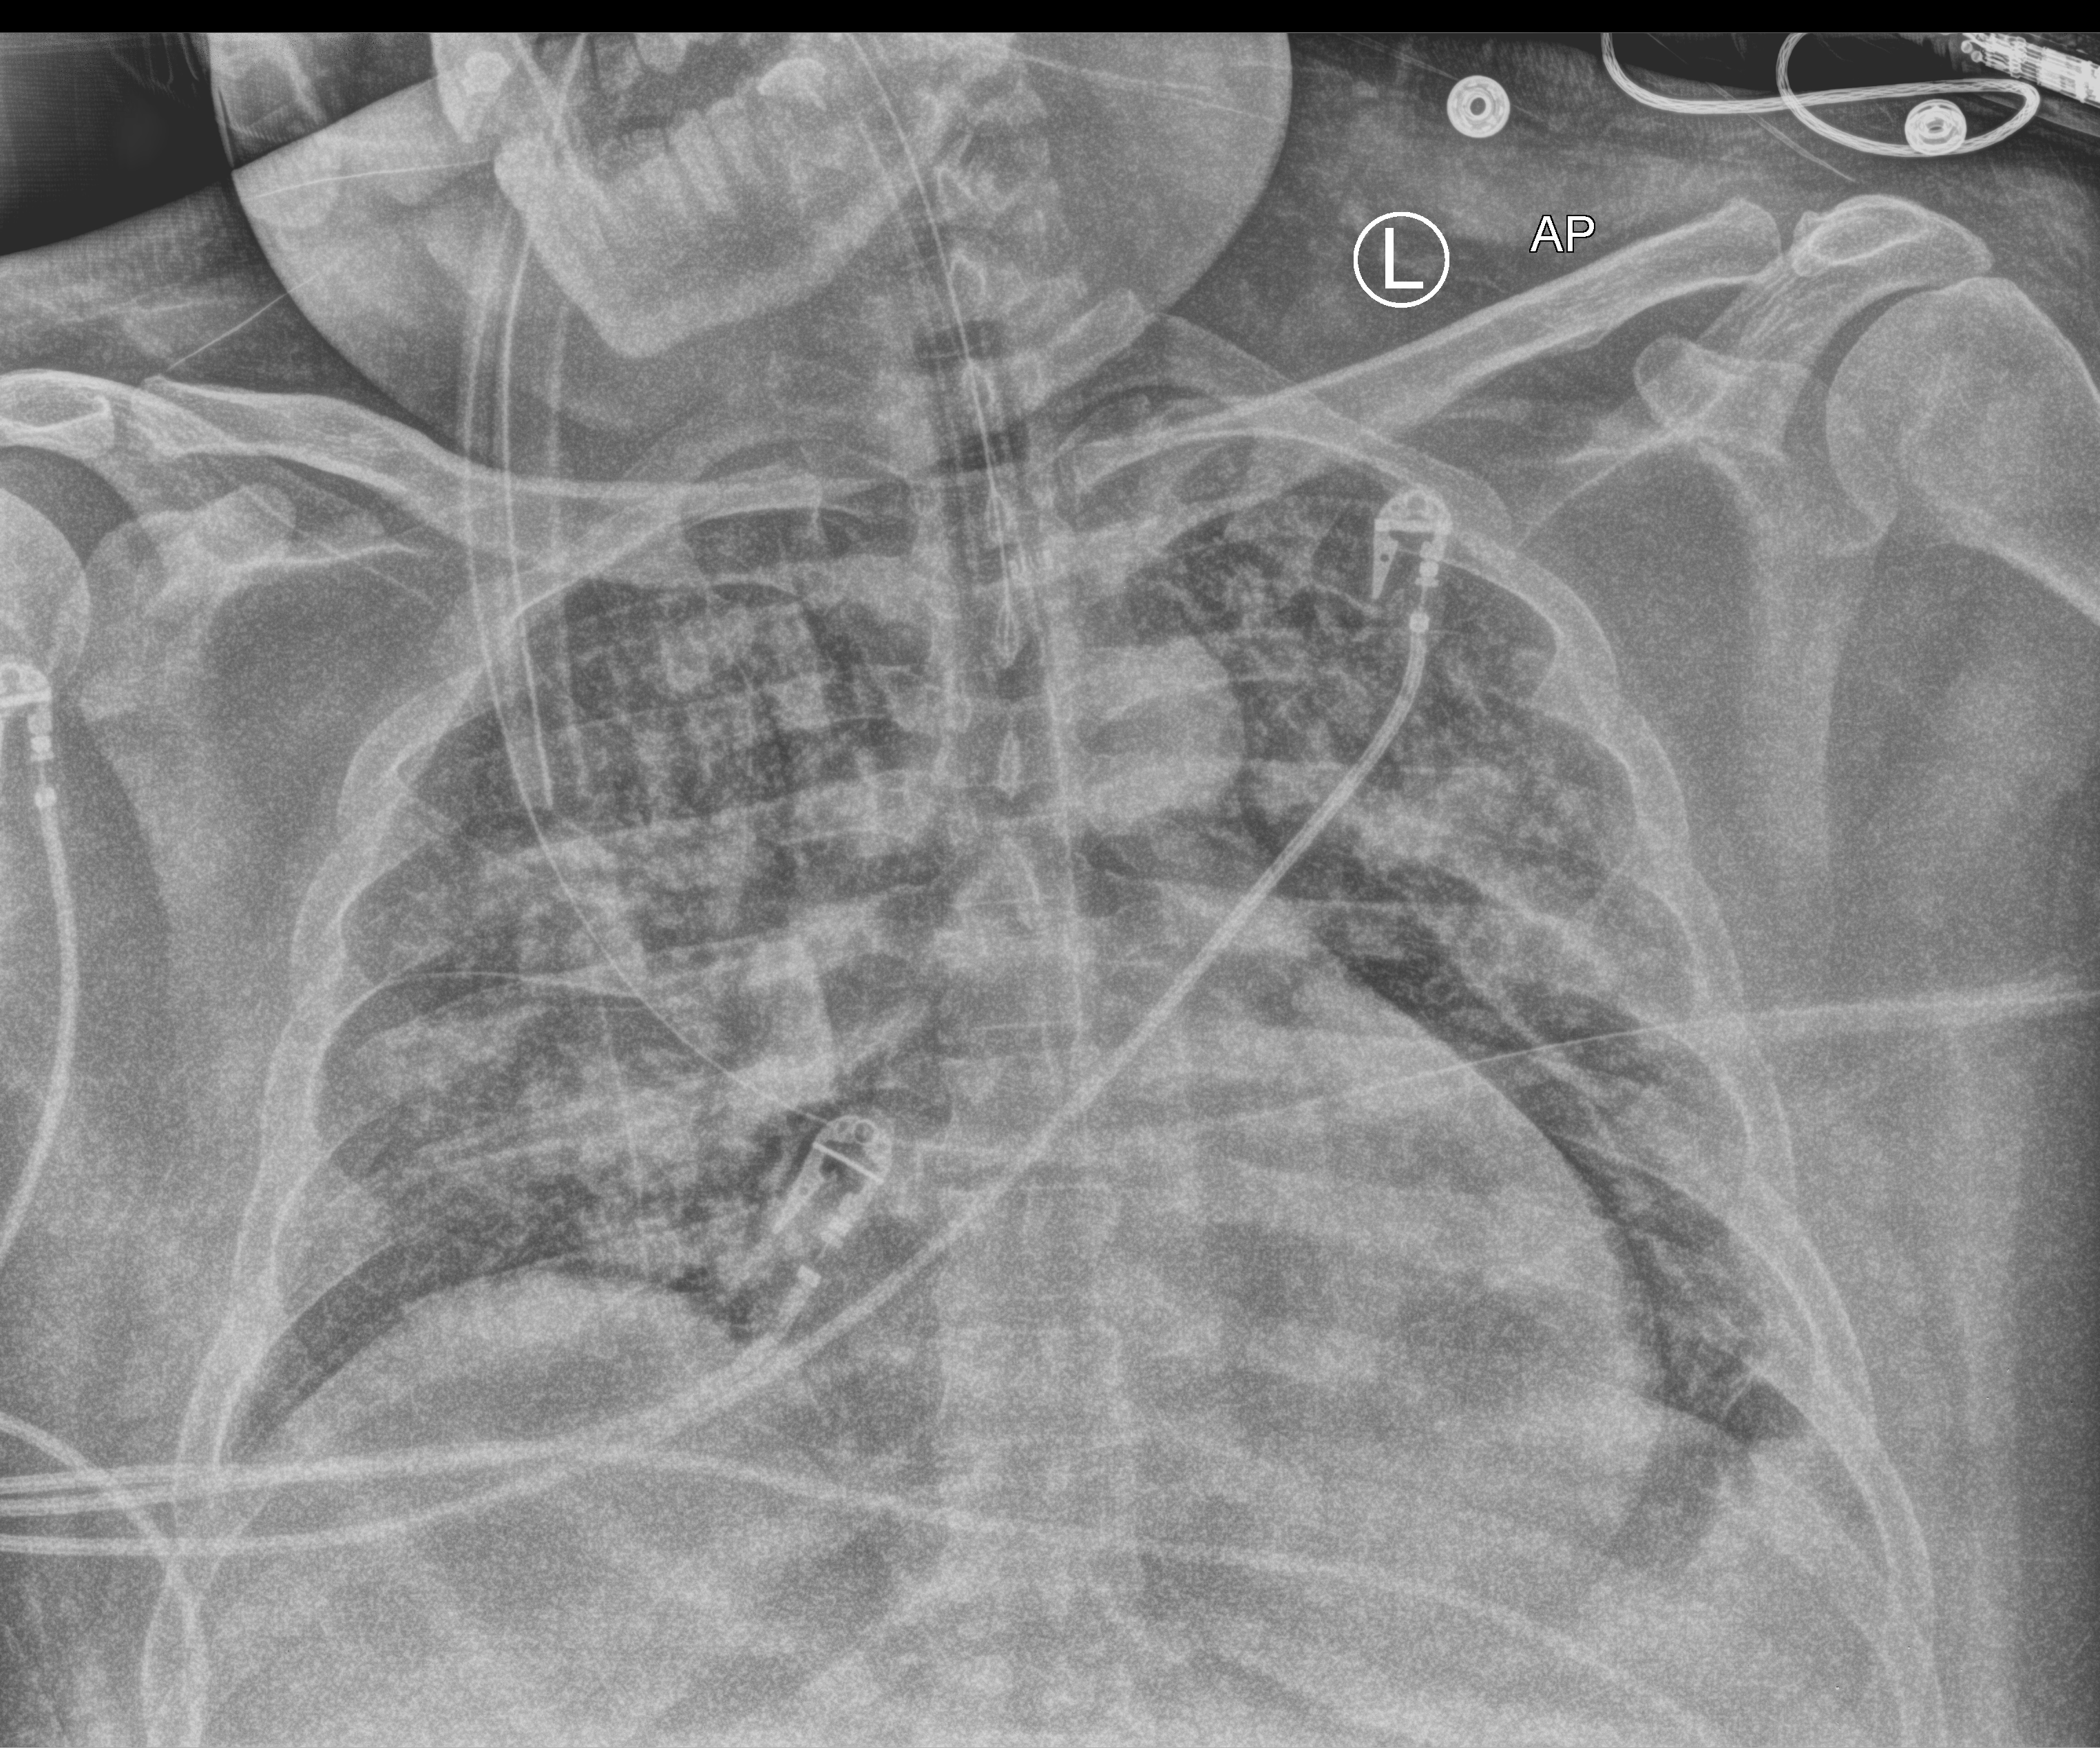
Bedside chest radiograph (computed radiography); anteroposterior (AP) projection. Adult patient hospitalised with COVID-19, age 18–59 years.
Admission-level facts for this patient (not findings on this image; timing relative to this image not recorded): other chronic lung disease (admission record): yes.